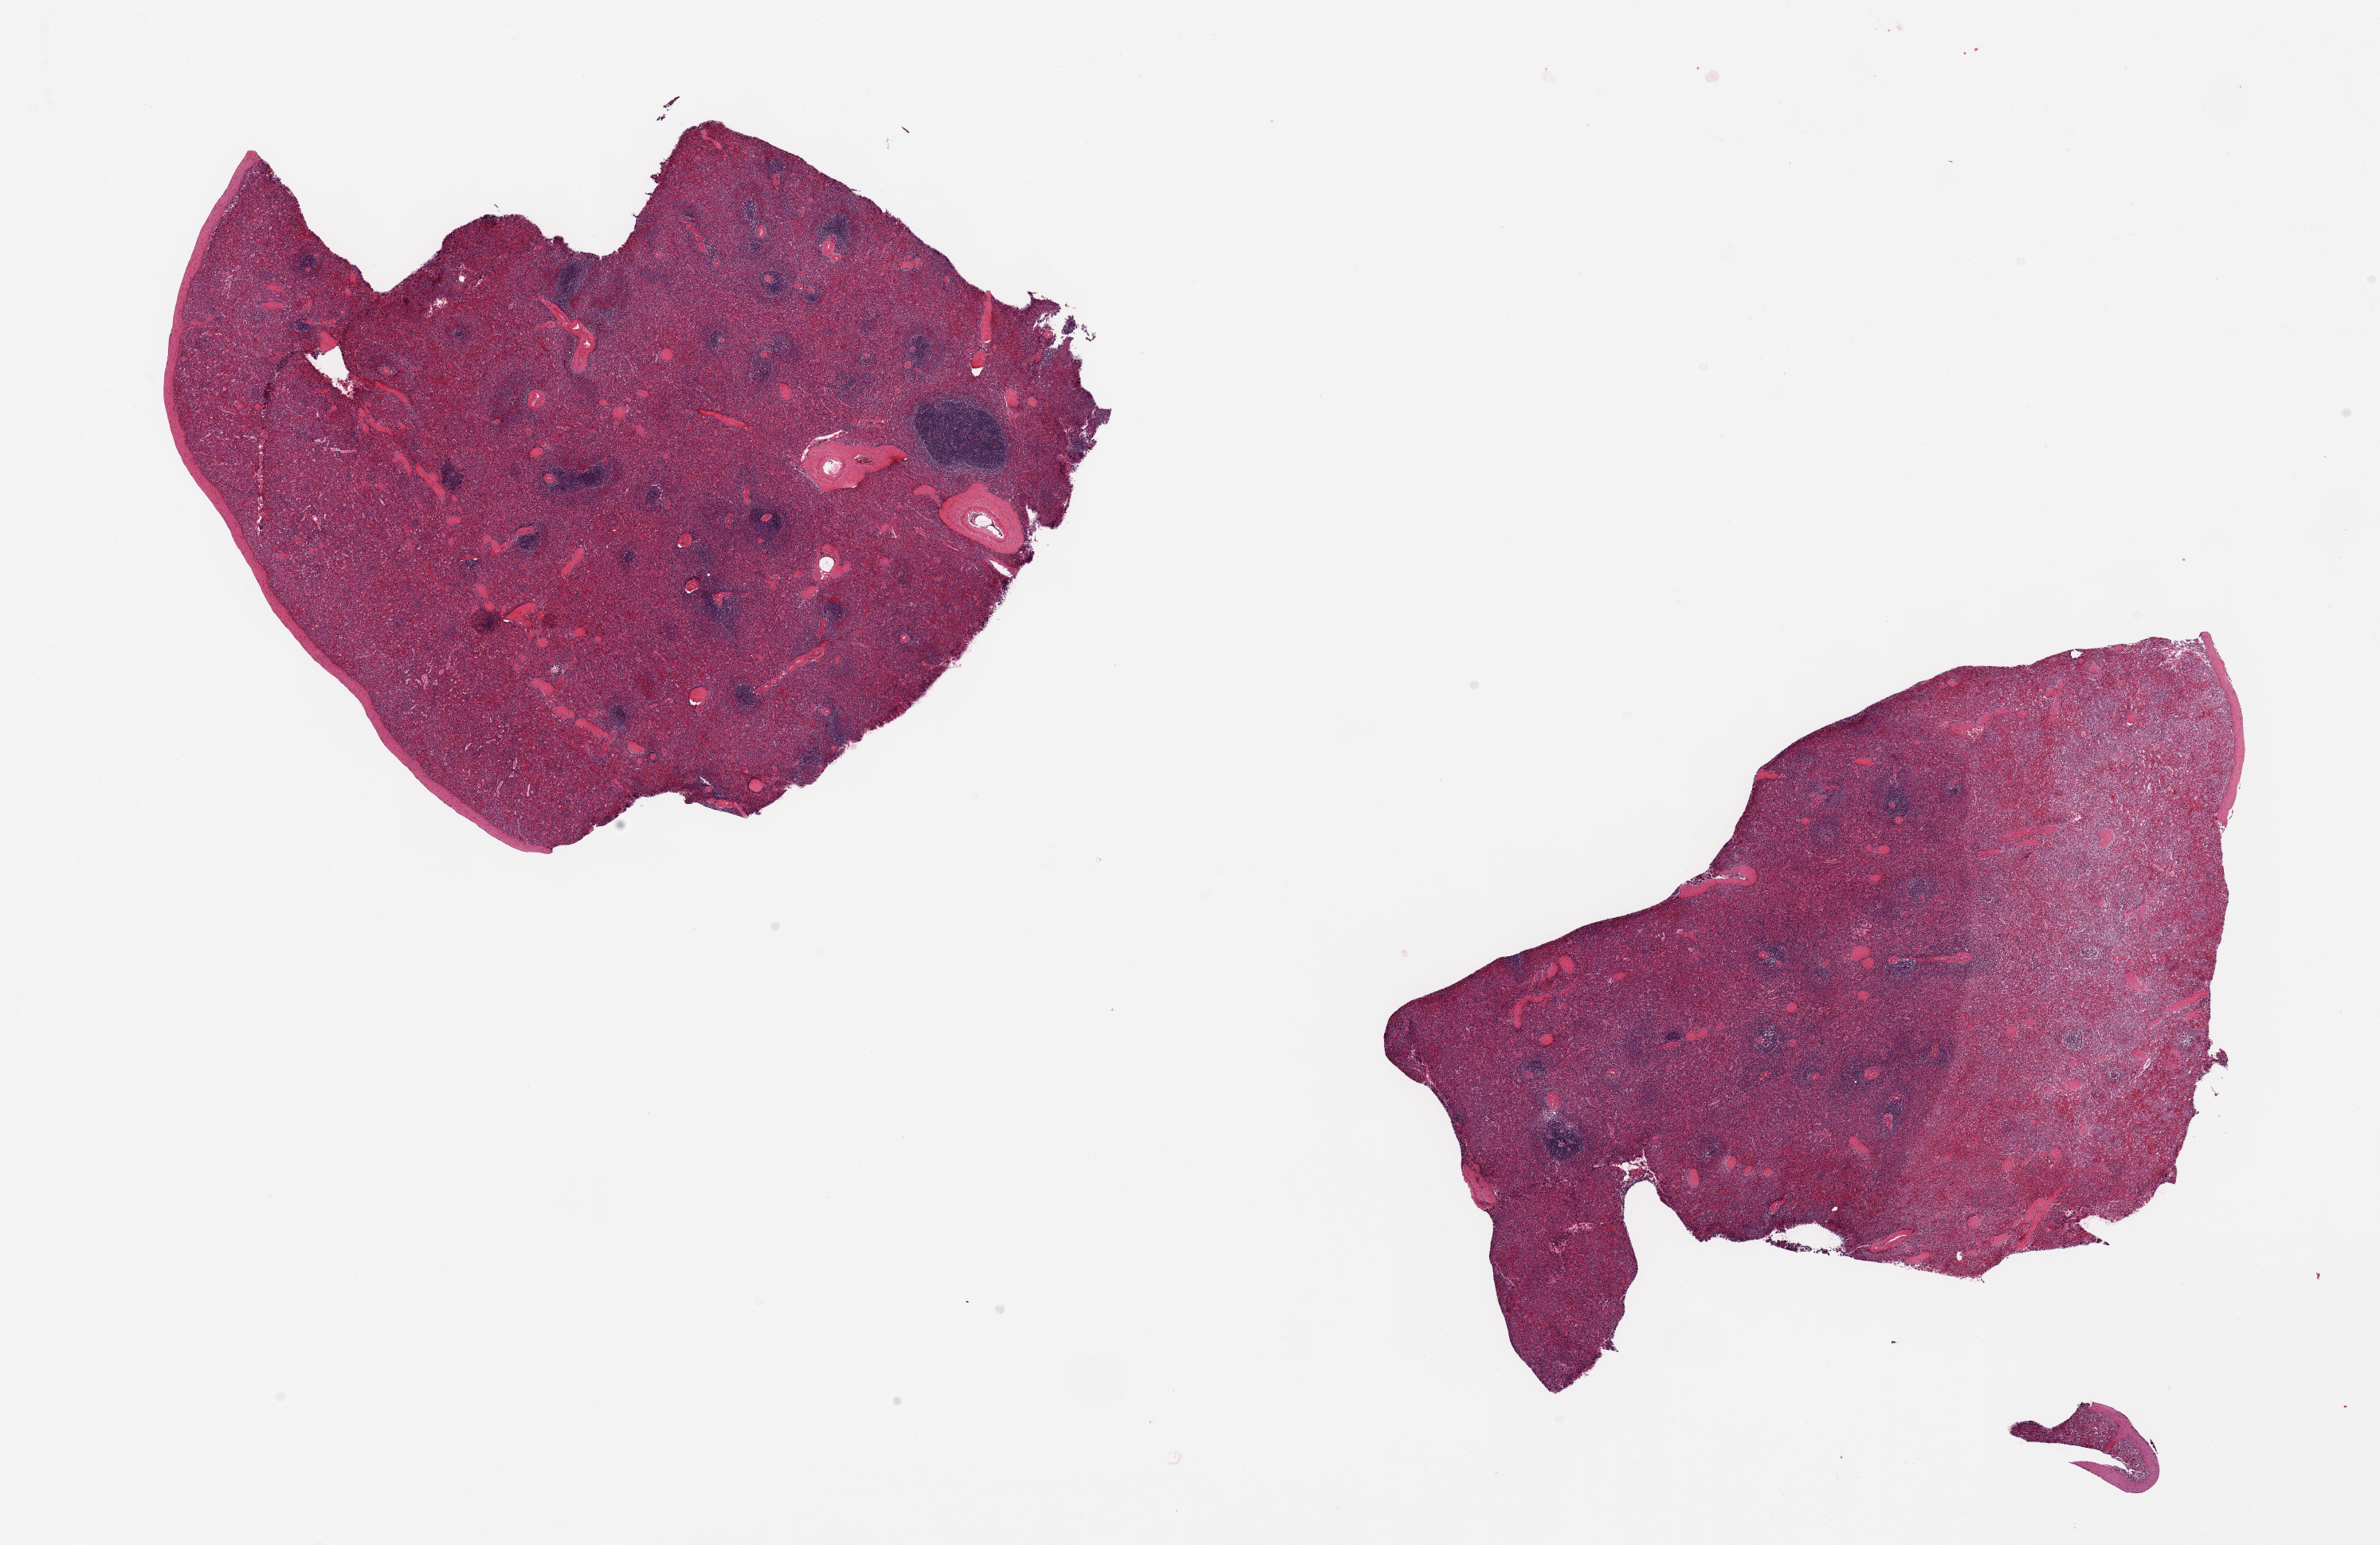
Digitized hematoxylin and eosin (H&E)-stained section, a low-resolution overview of the entire scanned area, about 23.6 x 15.3 mm (from a 20x scan); PAXgene-fixed, paraffin-embedded tissue; section of spleen (target tissue); donor tissue sample.
• reviewer comment on this tissue sample: 2 ~9x6 mm pieces. Capsule present